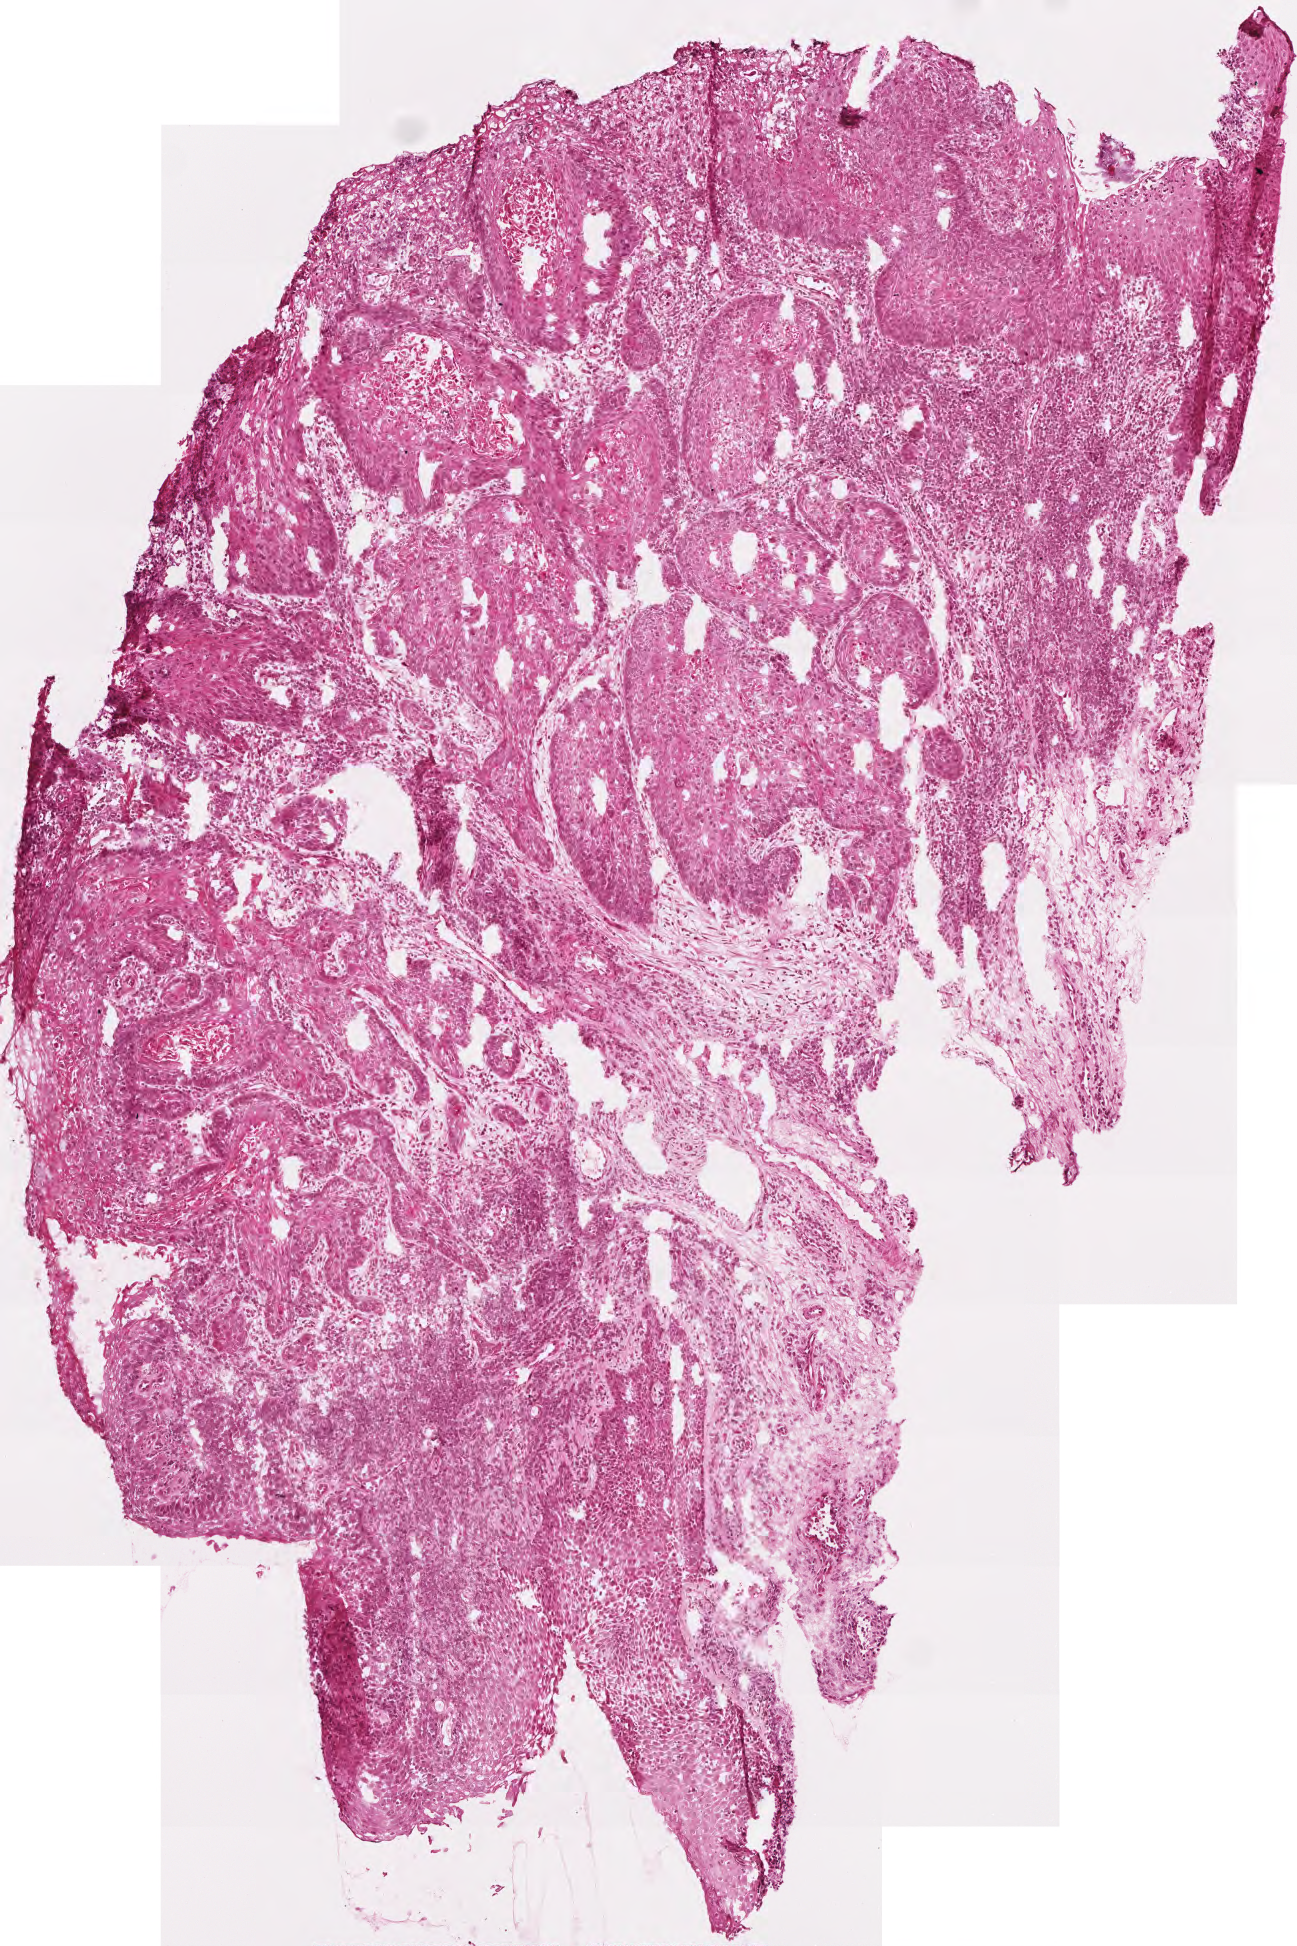
Digitized H&E-stained tissue section (whole slide) — a low-resolution overview of the entire scanned area, about 2.6 x 3.9 mm. Frozen section from the top of the tissue portion. Primary tumour sample from the head and neck. Female, age 70 years at initial diagnosis. Histologic grade: G2 (moderately differentiated). Composition of this section per pathologist review: tumour cells 85%, tumour nuclei 70%, normal cells 0%, stromal cells 15%, necrosis 0%.
• pathologic diagnosis: Squamous cell carcinoma, NOS (larynx, NOS)